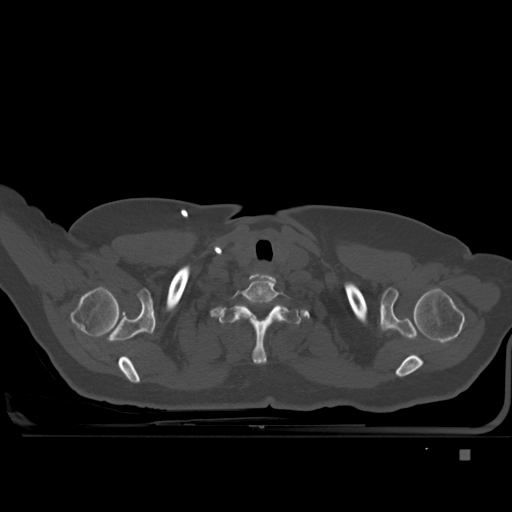
CT including the spine, one axial slice. Bone window (W 1800 / L 400 HU). 1.5 mm slice thickness. 512 × 512 image matrix. Female patient, age 74 years. Case-level facts recorded for this patient, not image findings: primary cancer: colon.
Outlined on this slice (semi-automatically segmented with operator editing):
- T1 vertebra: box from (x=233, y=300) to (x=287, y=365) px